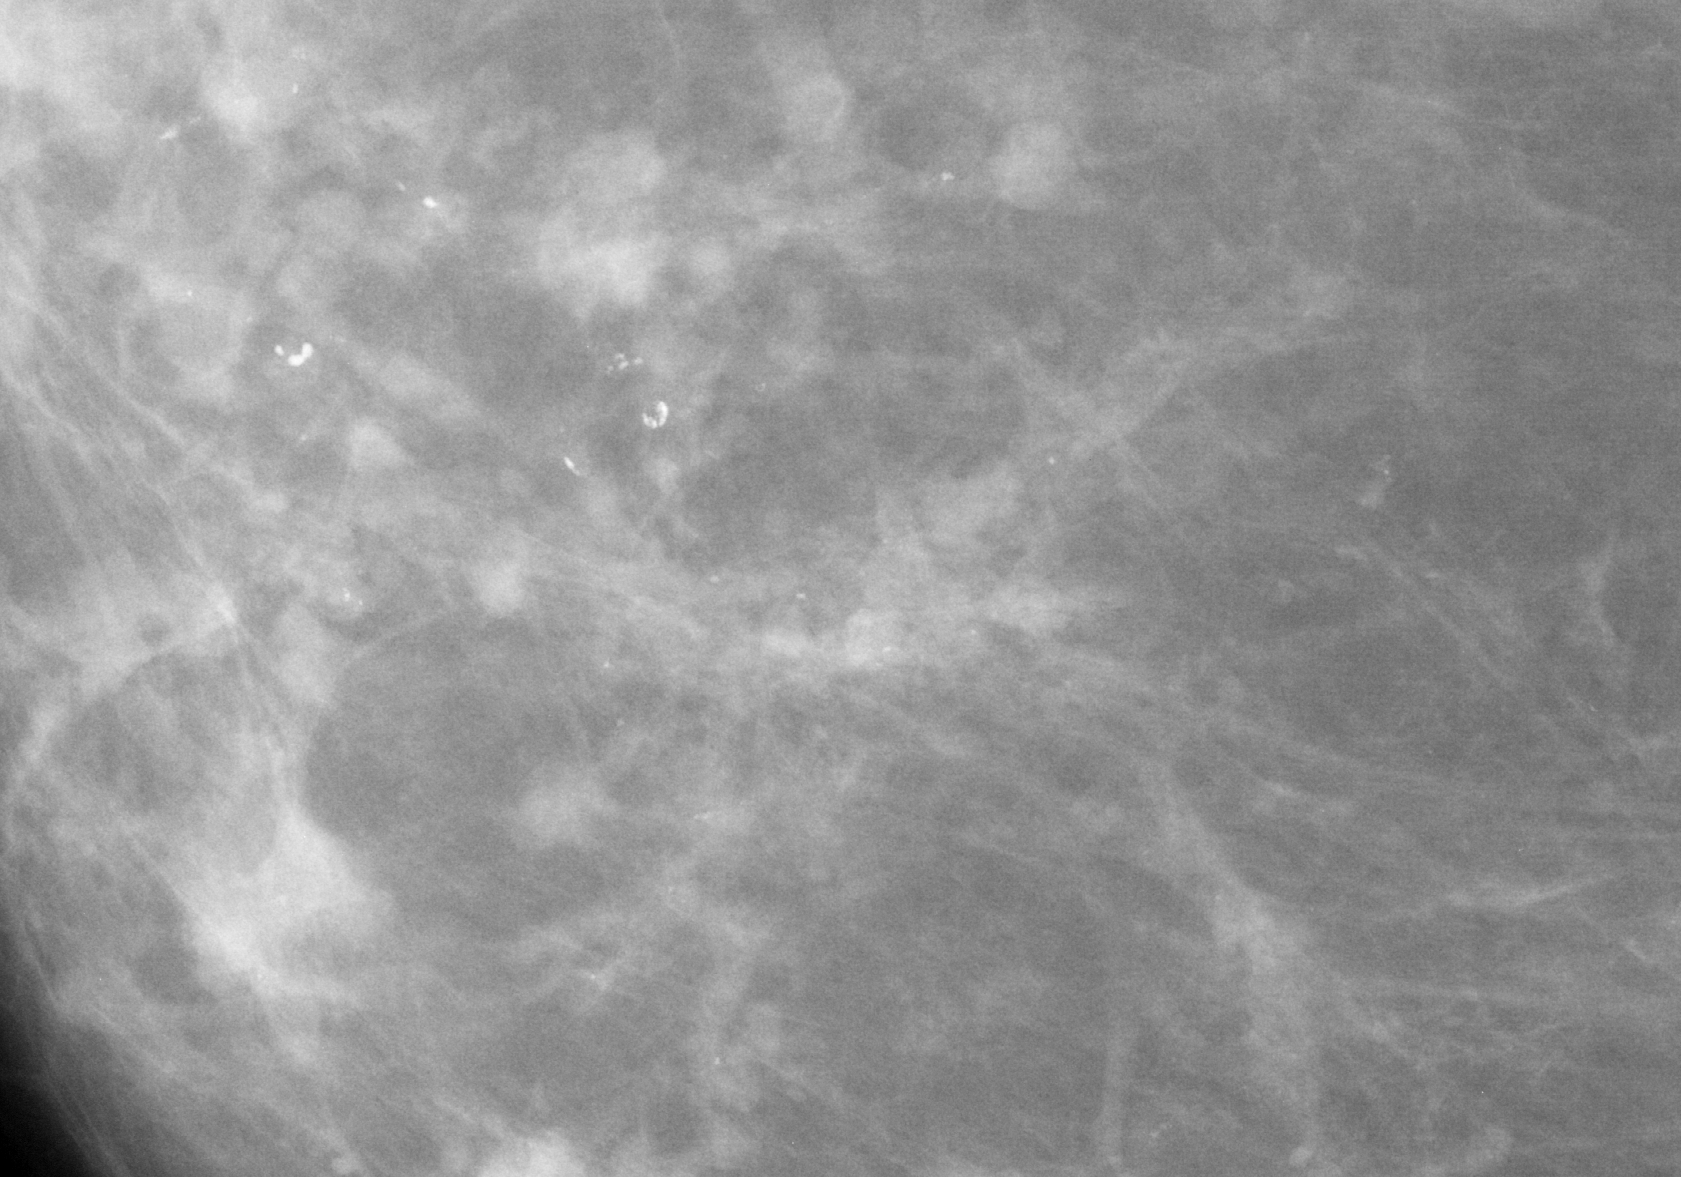
Region of interest cut from a scanned film mammogram (one marked finding), right breast, CC view, BI-RADS breast density category 2 (scale 1–4).
- Marked abnormality: calcifications, morphology pleomorphic, distribution segmental; BI-RADS assessment category 4; pathology result (as recorded, not read from the image): malignant.